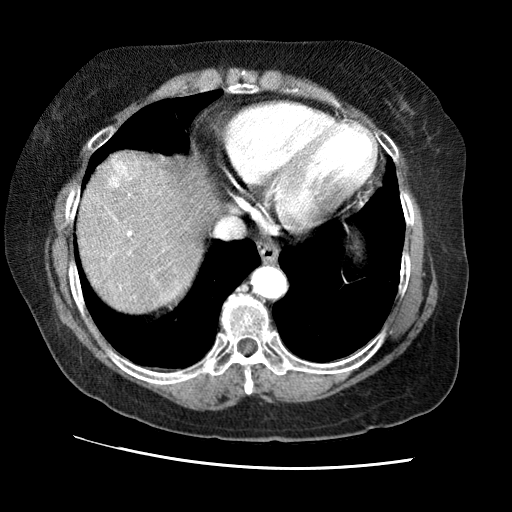
Contrast-enhanced abdominal CT (liver protocol), one axial slice. Reconstruction kernel STANDARD. 120 kVp. Soft-tissue window (W 400 / L 40 HU). 2.5 mm slice thickness. 512 × 512 image matrix, field of view 340 × 340 mm. From the clinical record (not read from this slice): diagnosis: hepatocellular carcinoma (patient treated with transarterial chemoembolisation; whether this scan precedes or follows treatment is not stated here); TNM stage (as recorded): Stage-II; Child-Pugh class: A; tumour differentiation: no biopsy.
Structures marked on this image (semi-automatic segmentation, software-assisted and operator-edited):
- liver parenchyma outside the tumour (the mass and vessels are separate outlines, so this box may not span the whole liver): box from (x=78, y=150) to (x=217, y=312) px
- mass: (x=101, y=151)–(x=141, y=190)
- liver vessels: (x=109, y=194)–(x=132, y=288)